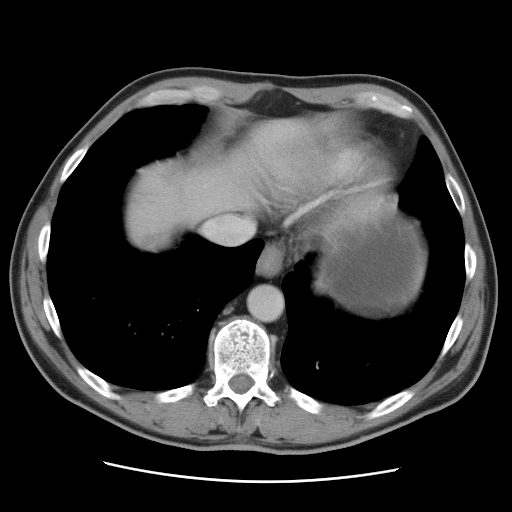
Contrast-enhanced abdominal CT, one axial slice; slice 81 of 89 in the series (ordered by position); intravenous contrast given; soft-tissue window (W 400 / L 40 HU); 5 mm slice thickness; 512 × 512 image matrix, field of view 366 × 366 mm. Male patient, age 59 years. Case-level facts recorded for this patient, not image findings: diagnosis: colorectal cancer liver metastases, imaged before liver resection; multiple liver metastases: yes; largest metastasis: 0.6 cm; disease in both lobes: yes.
Annotated regions visible in this slice (outlined manually by an expert reader):
- liver: bounding box <122,119,306,252> (left, top, right, bottom; pixels)
- planned liver remnant (the part of the liver to remain after resection): <151,119,306,221>
- liver metastasis: <142,235,165,252>